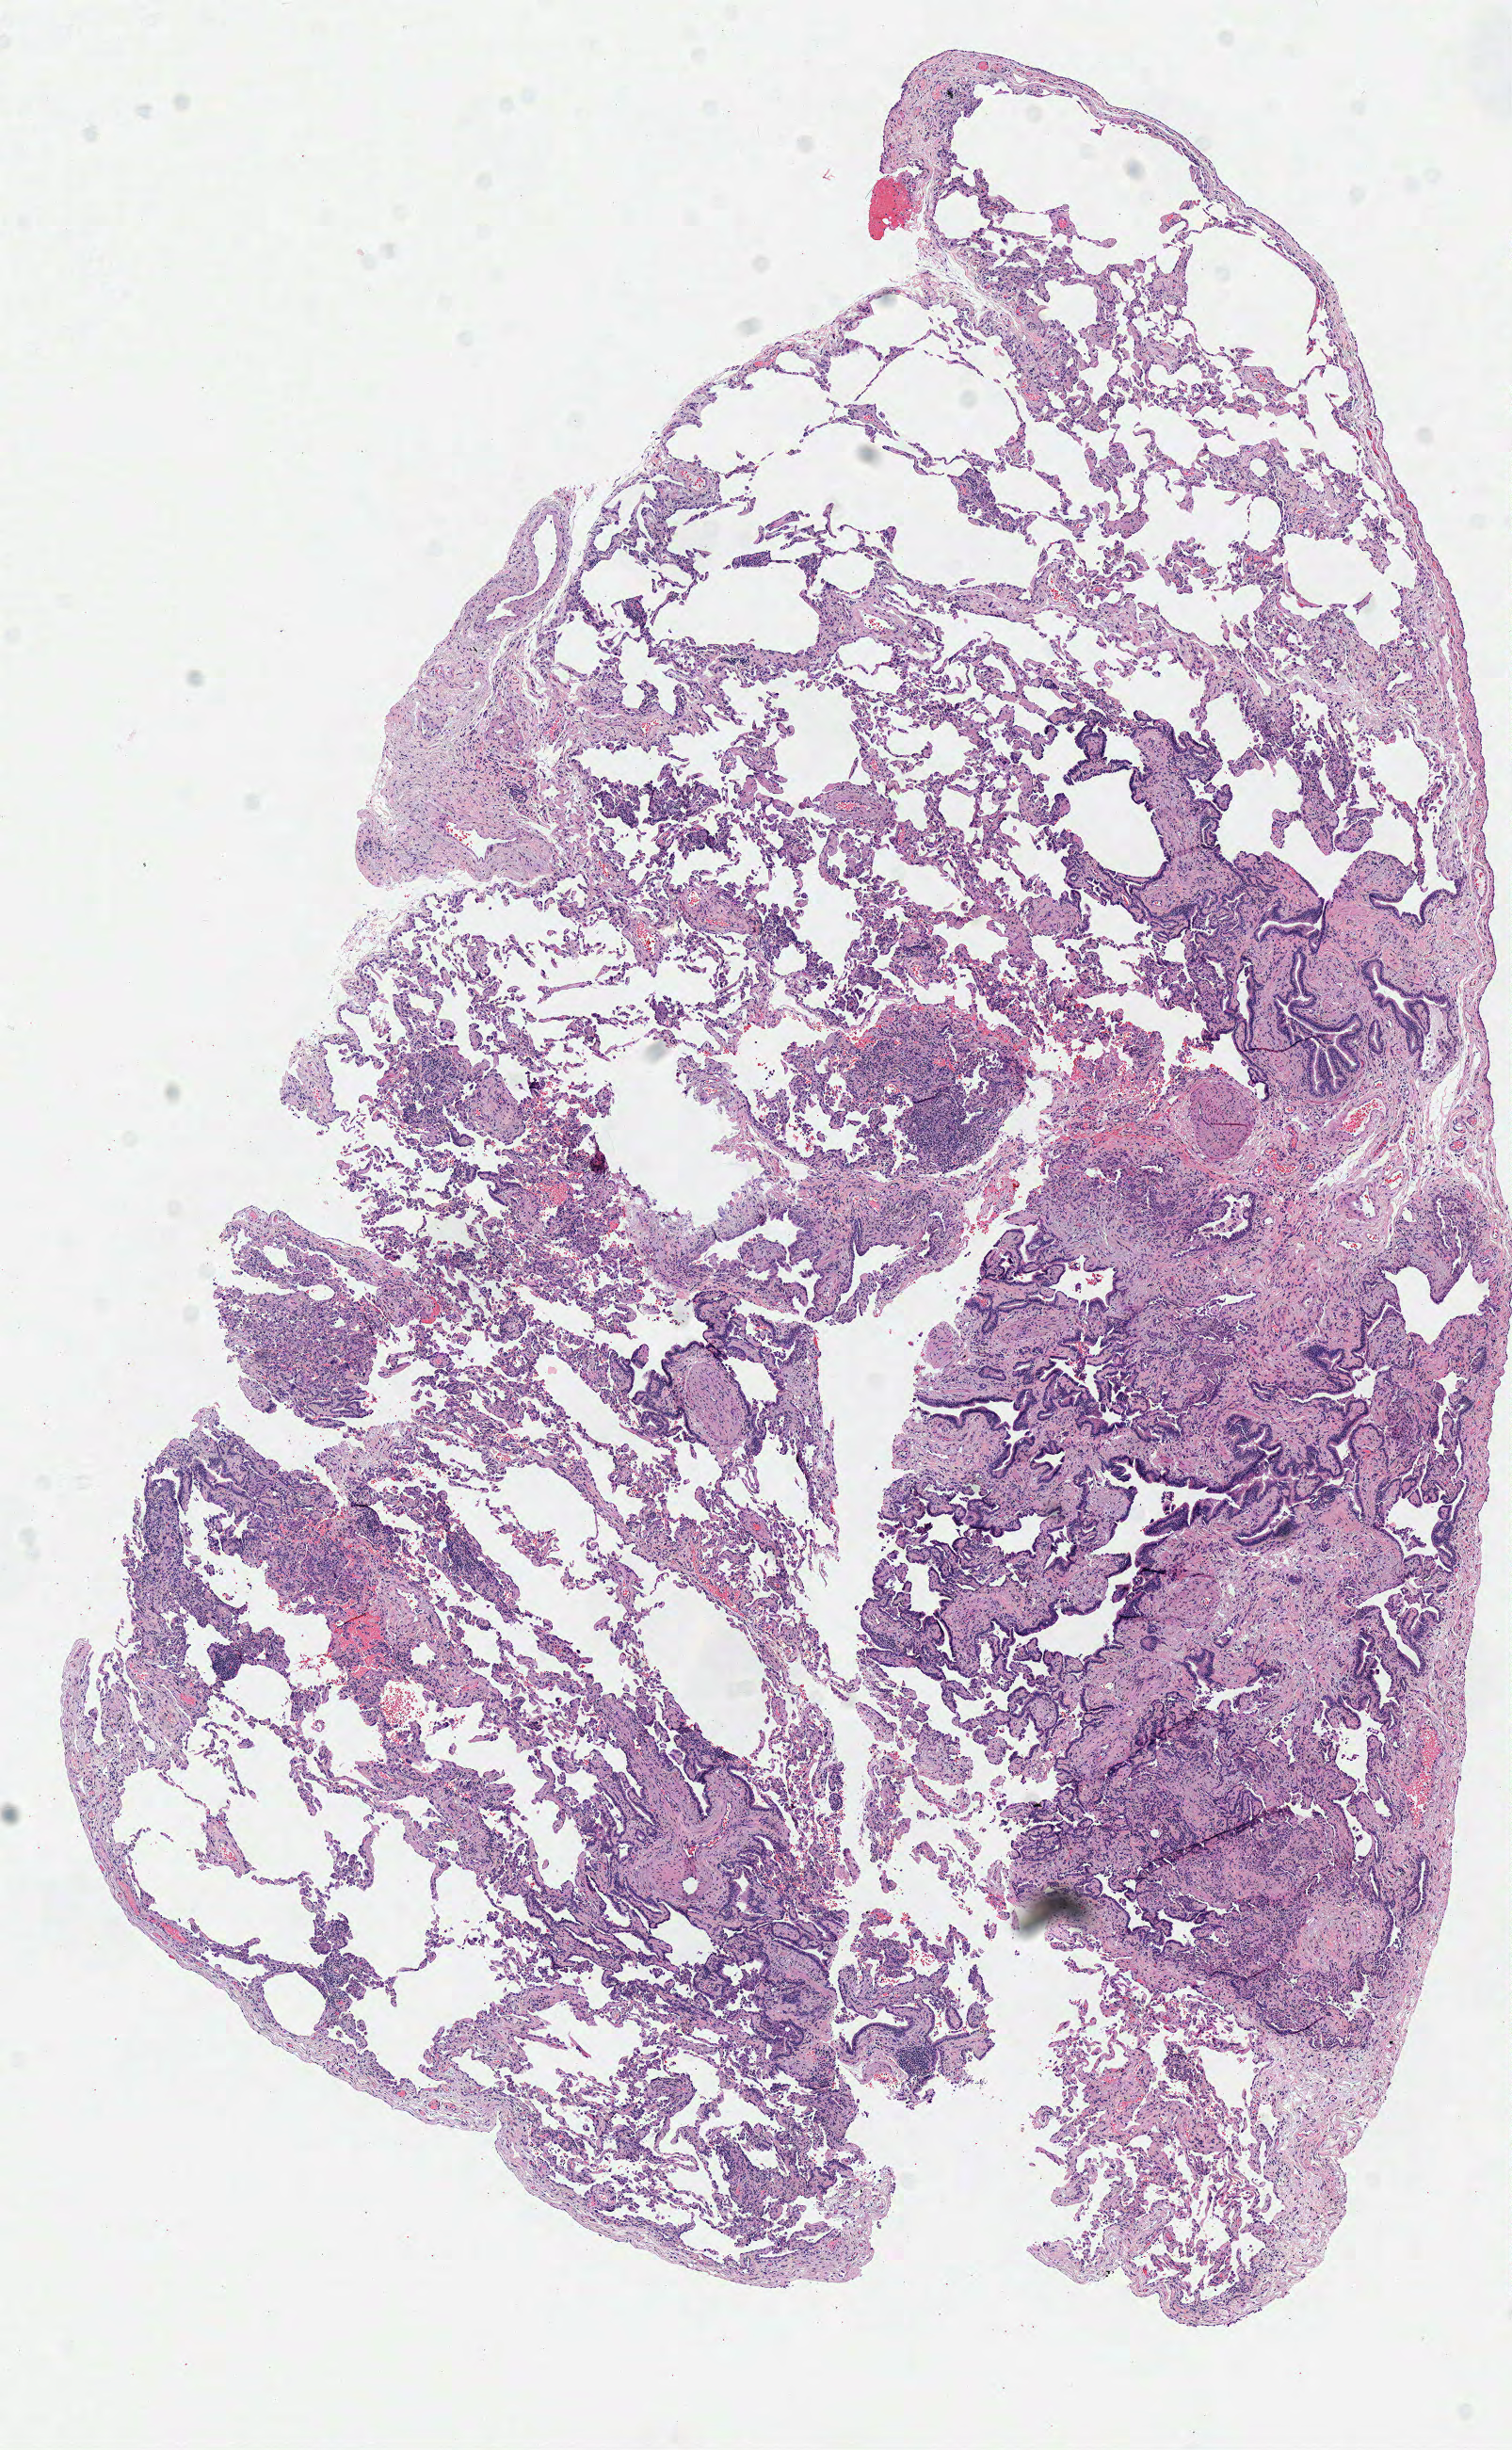
Whole-slide histology image, H&E-stained — shown as a low-resolution overview of the whole scanned area (about 6.3 x 10.3 mm, acquisition: 40x scan). Frozen section from the top of the tissue portion. Sample: solid tissue normal (non-tumour tissue), lung. Patient: female, age at initial diagnosis 81 years.
• this section: solid tissue normal sample (biorepository sample class)
• patient diagnosis: Adenocarcinoma, NOS (lower lobe, lung)